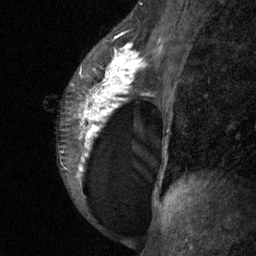
Breast MRI (dynamic contrast-enhanced), one sagittal slice; slice 42 of 64 in the series (ordered by position); dynamic contrast-enhanced study with each time point stored as its own series, time point 2 of 3 at this slice position (early post-contrast, ordered by acquisition time); 1.5 T; TE 4.8 ms, TR 27 ms; 2 mm slice thickness; 256 × 256 image matrix. Patient: female, 34 years. From the clinical record (not read from this slice): setting: breast cancer imaged before/during neoadjuvant chemotherapy; receptor status: HR-positive, HER2-negative.
Annotated regions visible in this slice (semi-automatic segmentation, software-assisted and operator-edited):
- analysis volume of interest (the breast-tissue region the enhancement analysis was run in; not a lesion): bounding box (x1, y1, x2, y2) in pixels: (56, 23, 157, 197)
- tumour enhancement mask (voxels above the 90 % enhancement threshold inside the analysis volume of interest): (79, 37, 143, 170)